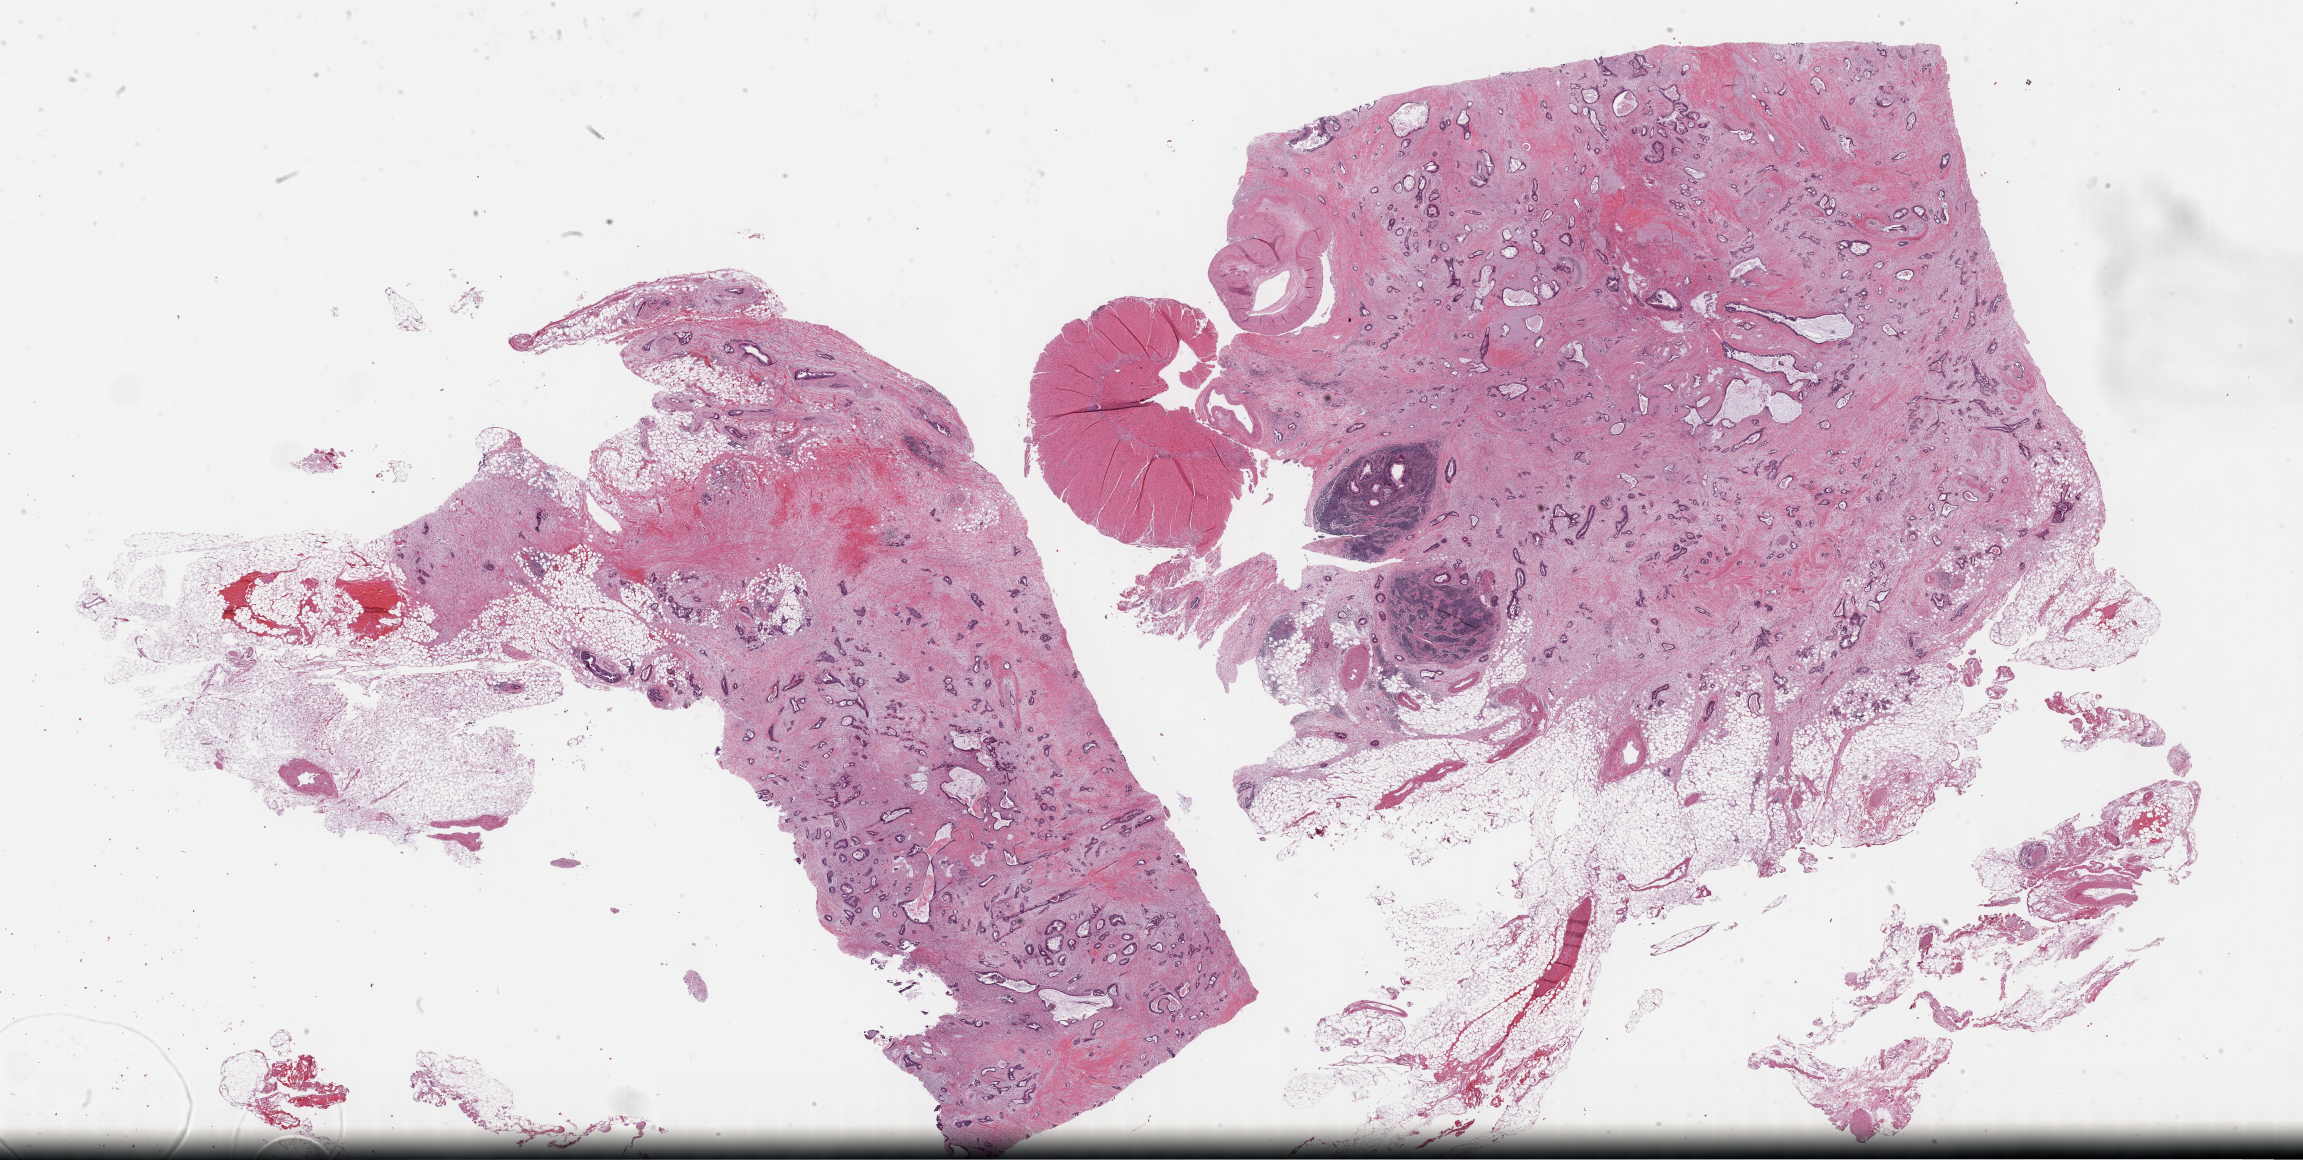
Whole-slide histology image, H&E, whole scanned area (about 37.2 x 18.8 mm, slide scanned at 40x) shown as a low-resolution overview, formalin-fixed paraffin-embedded (FFPE) diagnostic section, primary tumour sample from the pancreas. Male, age 74 years at initial diagnosis. Histologic grade: G4 (undifferentiated).
Lymph nodes positive (case pathology): 13 of 28 examined. AJCC pathologic stage: IIB (7th edition). Diagnosis: Infiltrating duct carcinoma, NOS (head of pancreas). TNM: T3 N1 M0.